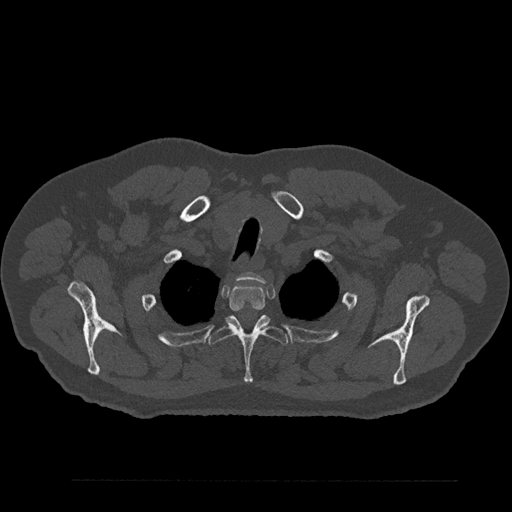
CT including the spine, one axial slice; 120 kVp; bone window (W 1800 / L 400 HU); 512 × 512 image matrix, field of view 430 × 430 mm. Male patient, age 61 years. Case-level facts recorded for this patient, not image findings: primary cancer: prostate.
Structures marked on this image (semi-automatic segmentation, software-assisted and operator-edited):
- T1 vertebra: bounding box <237,272,265,283> (left, top, right, bottom; pixels)
- T2 vertebra: <229,284,265,312>
- T3 vertebra: <208,315,289,384>